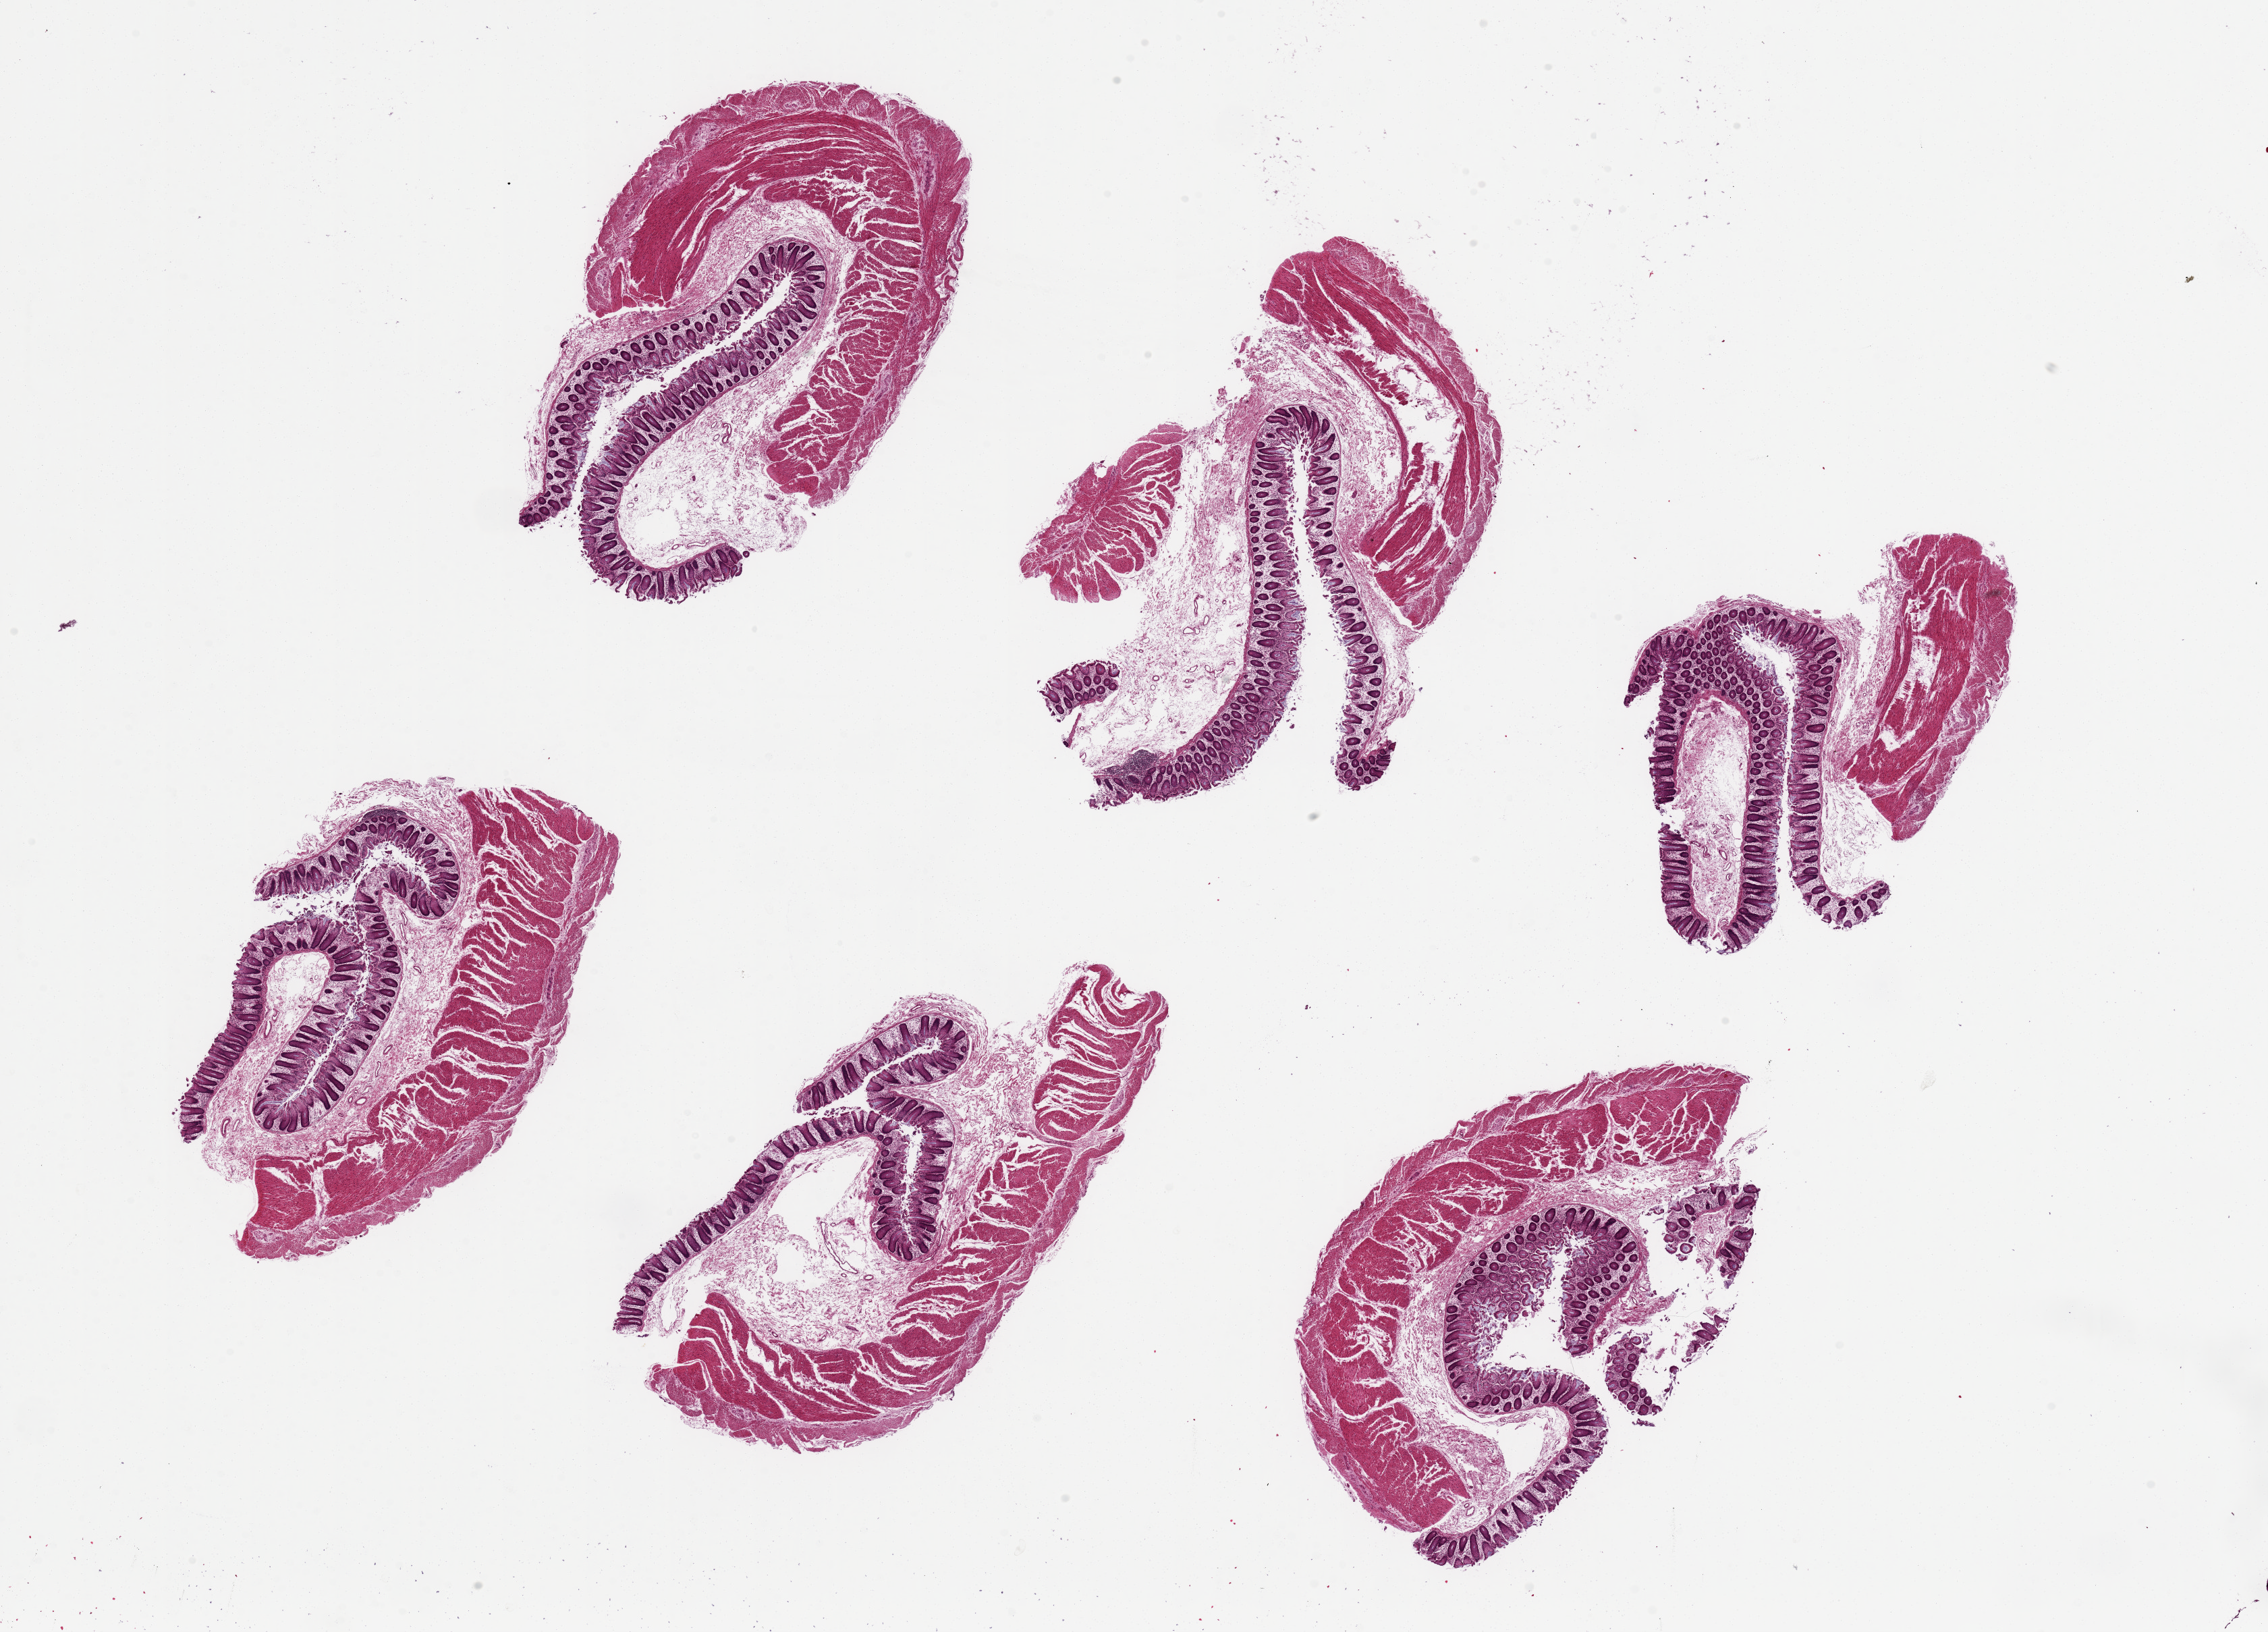
Digitized hematoxylin and eosin (H&E)-stained section, brightfield, shown as a low-resolution overview of the whole scanned area (about 26.6 x 19.1 mm, acquisition: 20x scan), PAXgene-fixed paraffin-embedded (PFPE) section, section of transverse colon (target tissue), donor tissue sample.
Review note (as recorded): 6 pieces up to 7x4 mm; surface sloughing.